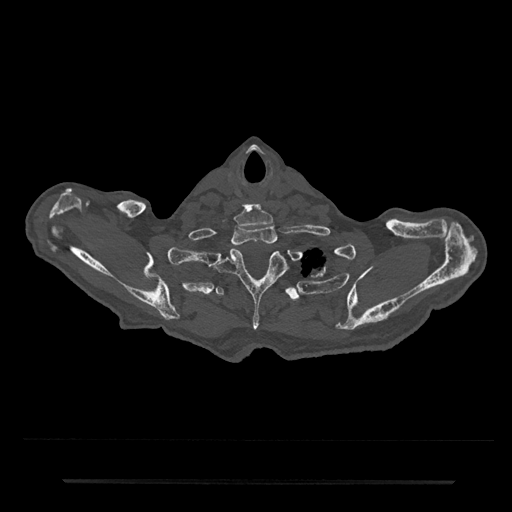
CT including the spine, one axial slice; position 701 of 797 along the scan axis; bone window (W 1800 / L 400 HU); 512 × 512 image matrix, field of view 427 × 427 mm. Patient: male, 74 years. Case-level facts recorded for this patient, not image findings: primary cancer: prostate.
Annotated regions visible in this slice (semi-automatic segmentation, software-assisted and operator-edited):
- T1 vertebra: box from (x=232, y=225) to (x=277, y=245) px
- T2 vertebra: (x=212, y=249)–(x=286, y=331)
- T3 vertebra: (x=215, y=286)–(x=300, y=302)